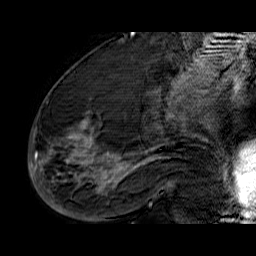
Breast MRI (dynamic contrast-enhanced), one sagittal slice; position 32 of 60 along the scan axis; dynamic contrast-enhanced series, time point 2 of 6 at this slice position (early post-contrast); 1.5 T; TE 6.5 ms, TR 32.9 ms; 256 × 256 image matrix. Female patient. From the clinical record (not read from this slice): setting: breast cancer imaged before/during neoadjuvant chemotherapy; receptor status: HR-positive, HER2-negative.
Annotated regions visible in this slice (semi-automatically segmented with operator editing):
- analysis volume of interest (the breast-tissue region the enhancement analysis was run in; not a lesion): bounding box [x1, y1, x2, y2] px = [33, 74, 176, 210]
- tumour enhancement mask (voxels above the 100 % enhancement threshold inside the analysis volume of interest): [33, 101, 154, 192]